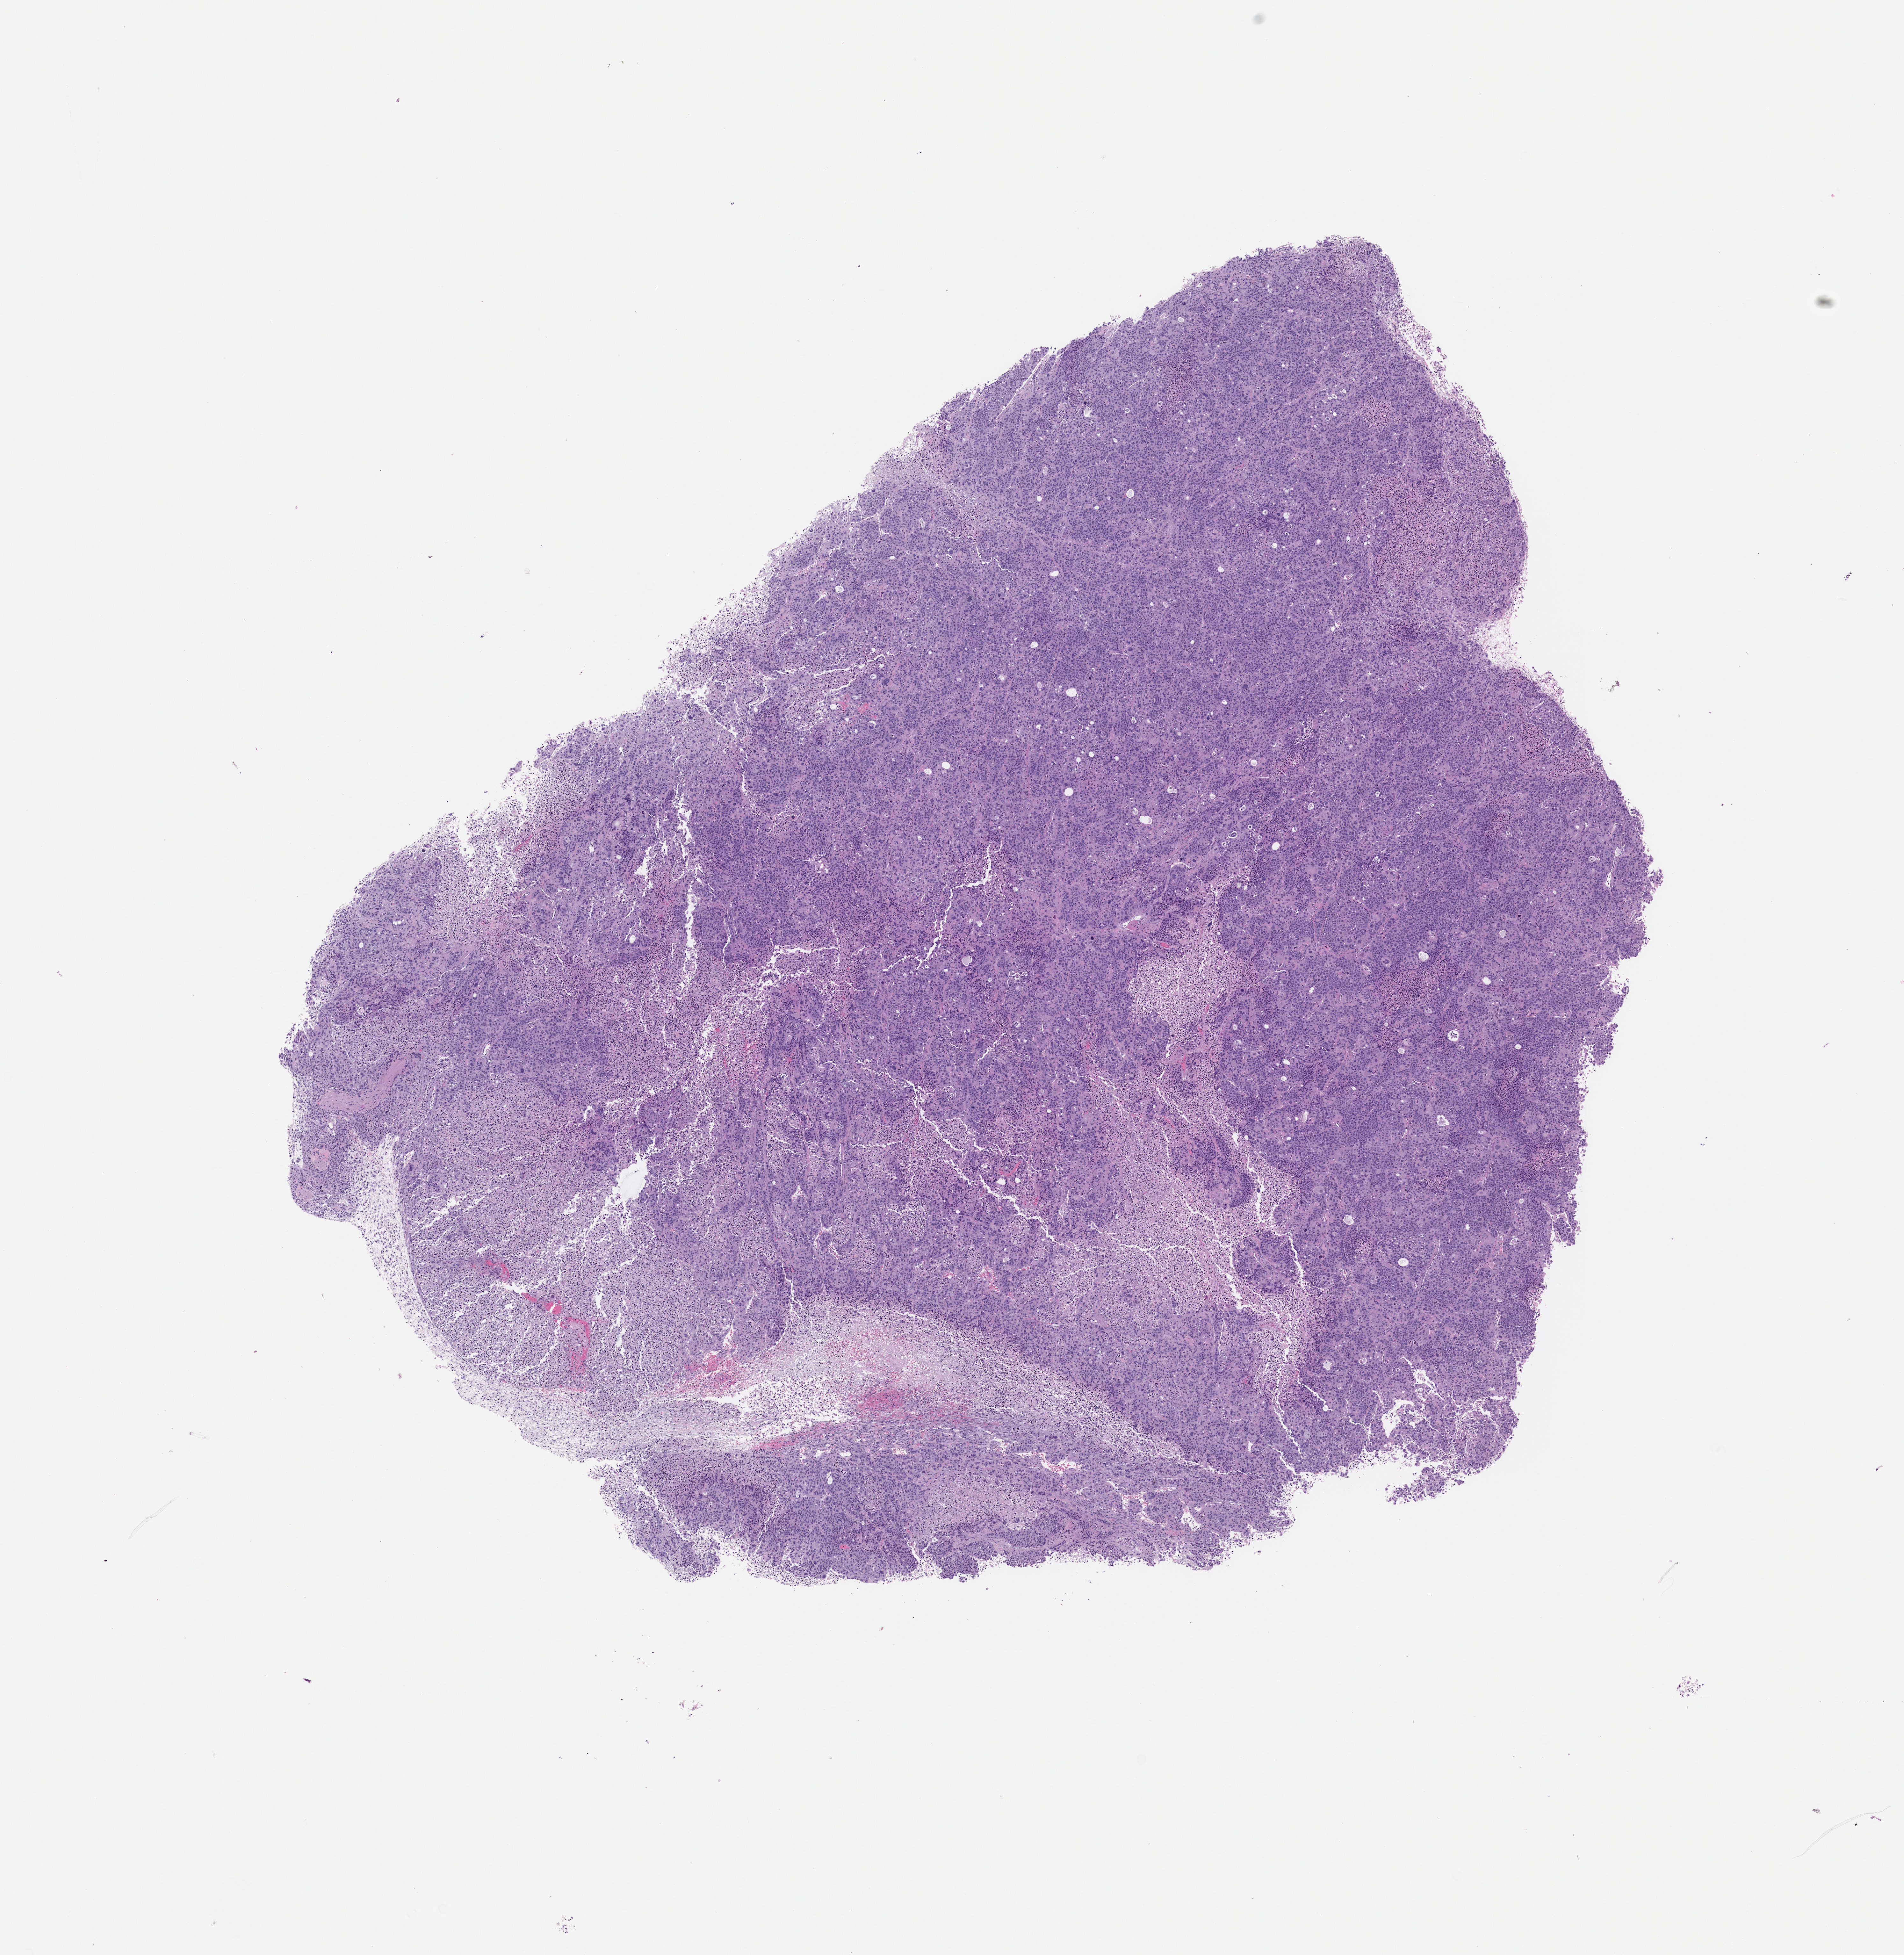
Whole-slide image, haematoxylin and eosin: patient-derived xenograft (human tumor grown in a mouse), passage 4, a low-resolution overview of the entire scanned area, about 12.0 x 12.3 mm. FFPE section. Originating tumor site category: bladder.
* originating patient diagnosis: Urothelial Carcinoma